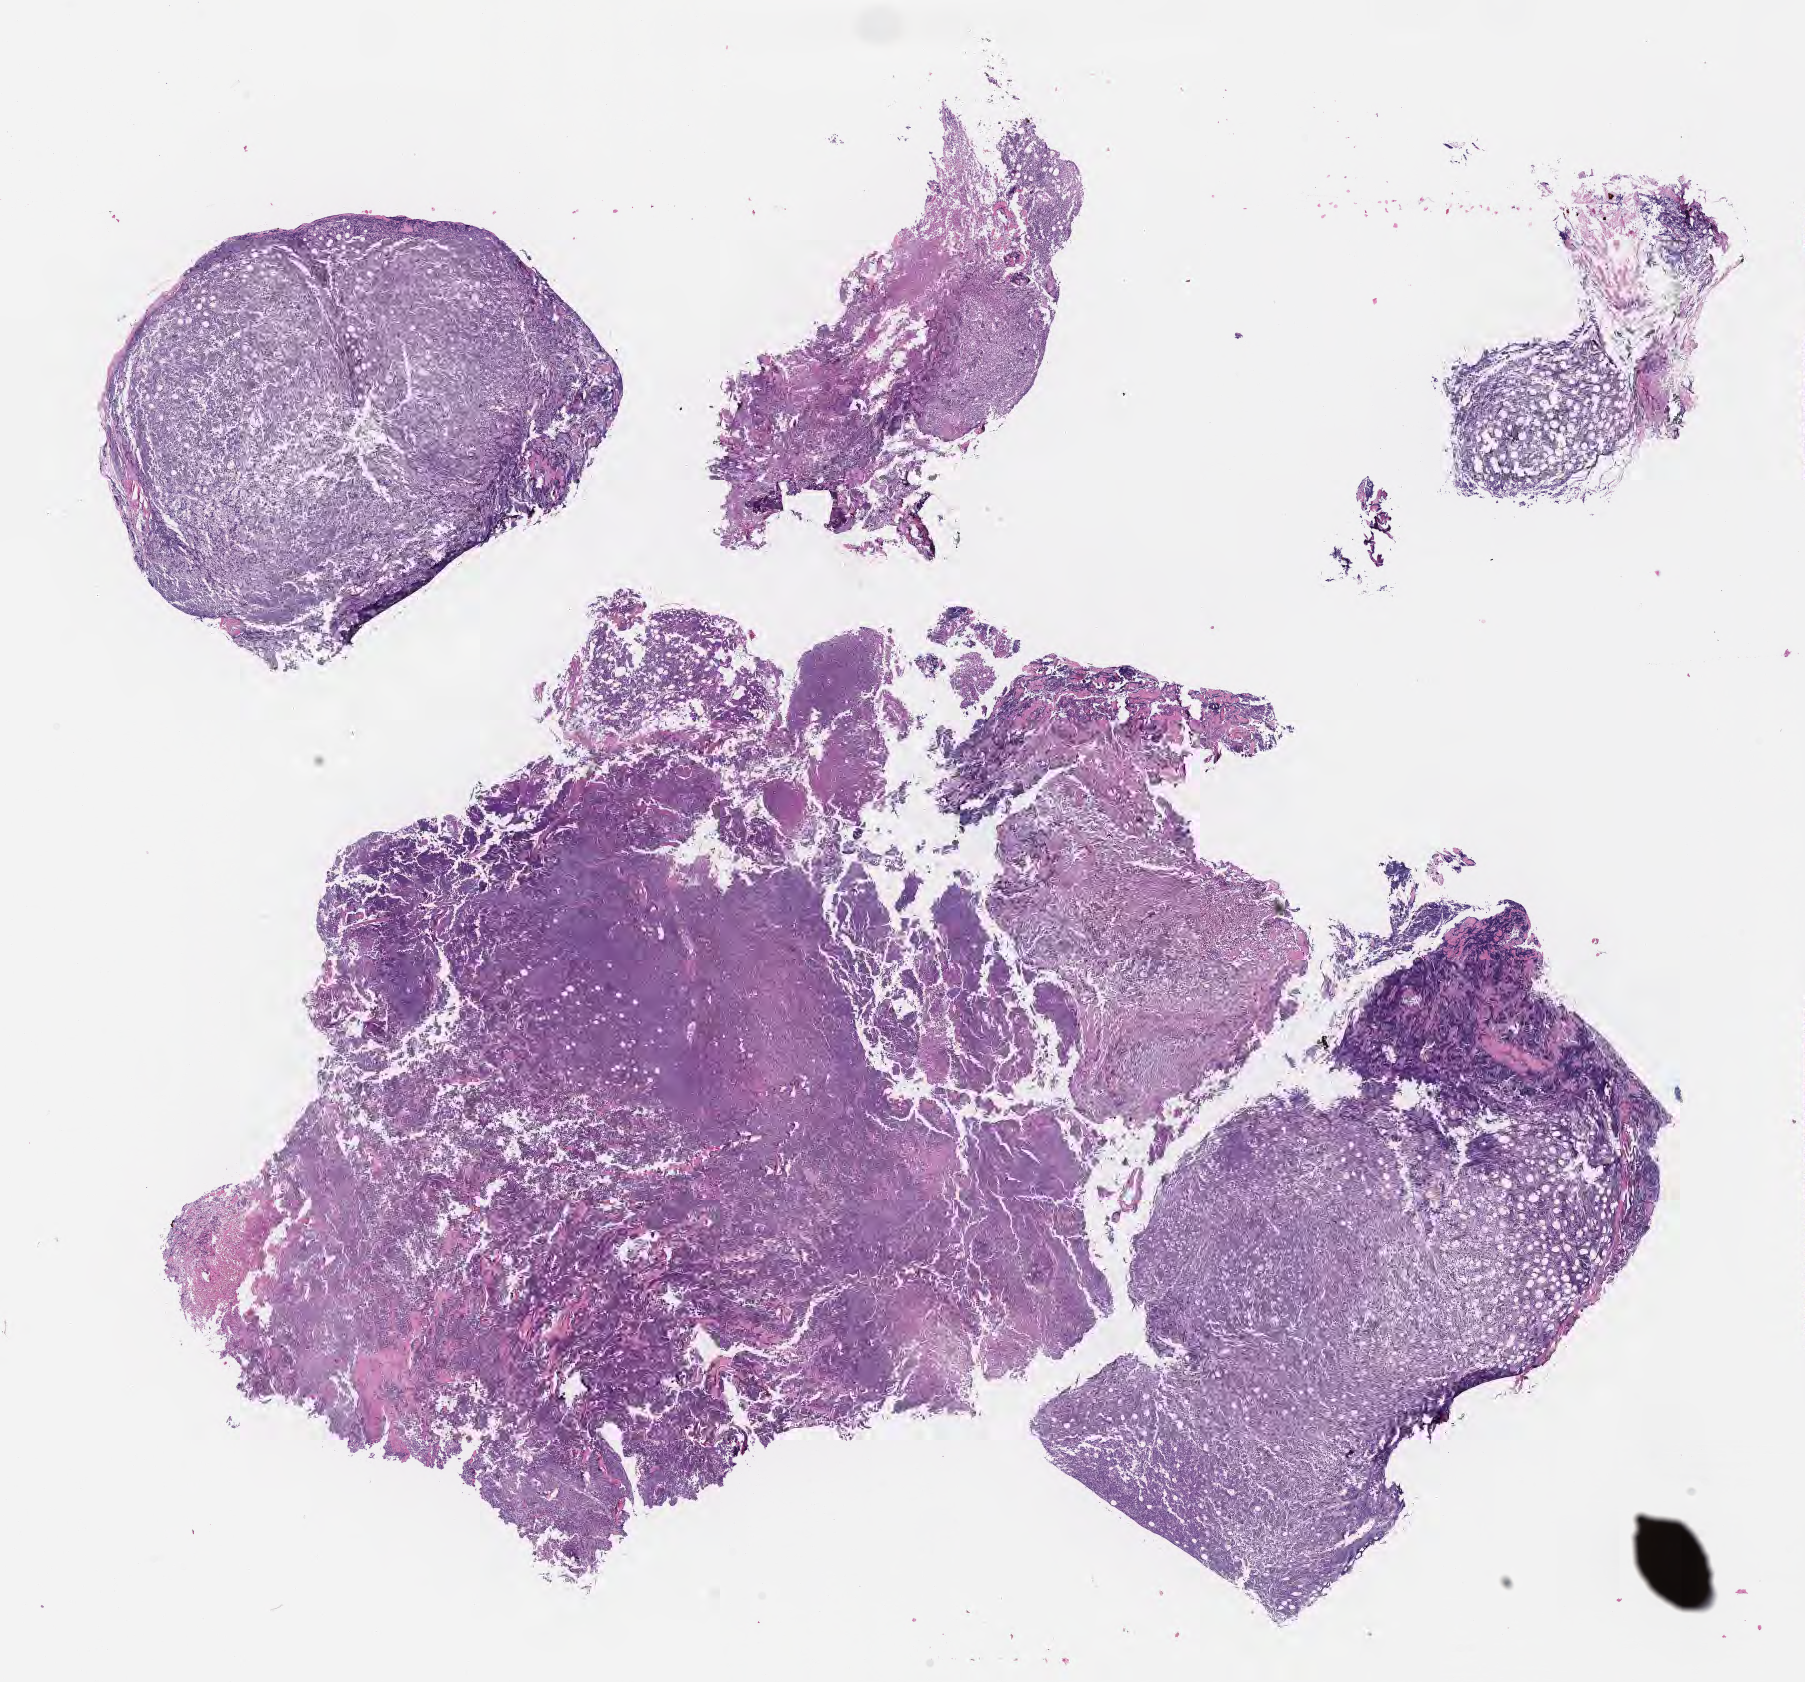
Whole-slide image, hematoxylin and eosin (H&E) stain, whole scanned area (about 14.6 x 13.6 mm) shown as a low-resolution overview. Specimen: tumor tissue. Male patient, aged 23.
Diagnosis: Burkitt lymphoma, NOS.